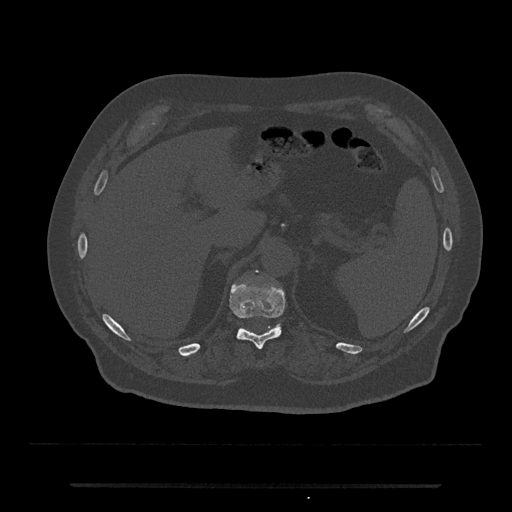
CT including the spine, one axial slice; position 642 of 797 along the scan axis; reconstruction kernel Br40s/3; bone window (W 1800 / L 400 HU); 0.5 mm slice thickness; 512 × 512 image matrix, field of view 434 × 434 mm. Patient: male, 80 years. Case-level facts recorded for this patient, not image findings: primary cancer: prostate; vertebrae with lytic lesions (as recorded): L1, T11.
Outlined on this slice (semi-automatic segmentation, software-assisted and operator-edited):
- T11 vertebra: box from (x=230, y=285) to (x=285, y=350) px
- T12 vertebra: (x=239, y=270)–(x=281, y=329)